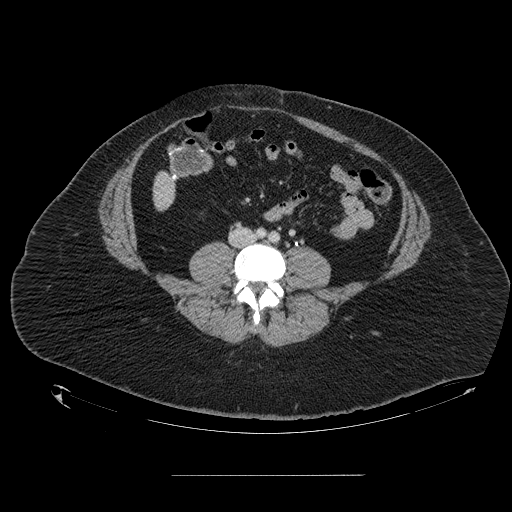
Contrast-enhanced abdominal CT, one axial slice; slice 11 of 164 in the series (ordered by position); 120 kVp; intravenous contrast given; soft-tissue window (W 400 / L 40 HU); 512 × 512 image matrix. Female patient, age 52 years. Case-level facts recorded for this patient, not image findings: diagnosis: colorectal cancer liver metastases, imaged before liver resection.
Structures marked on this image (outlined manually by an expert reader):
- liver: bounding box <154,174,176,209> (left, top, right, bottom; pixels)